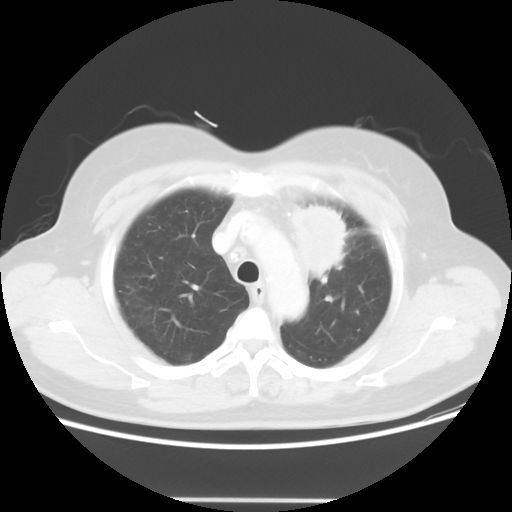
Chest CT, one axial slice. Slice 42 of 52 in the series (ordered by position). 120 kVp. Lung window (W 1500 / L -600 HU). 5 mm slice thickness. 512 × 512 image matrix, field of view 382 × 382 mm. Female patient, age 52 years. From the clinical record (not read from this slice): clinical TNM (as recorded): T2 N3 M0.
Annotated regions visible in this slice (rectangle marked by the reading radiologist):
- lung tumour (recorded histology: adenocarcinoma): box from (x=289, y=200) to (x=351, y=284) px